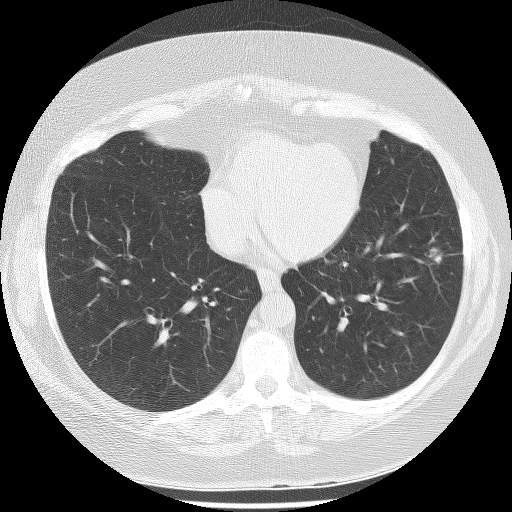
Axial slice from a low-dose chest CT screening exam. Baseline annual screen. Lung window (W 1500 / L -600 HU). 2.5 mm slice thickness. Lung (sharp) reconstruction kernel (BONE). Slice 136 of 233 in the series. Female participant, aged 56 years at enrolment. Former smoker at enrolment.
Expert reader's lesion annotation, bounding box (x1, y1, x2, y2) in pixels: (388, 222, 465, 287). The exam's reader record, not a measurement of the box and not confirmed to be the same lesion: non-calcified nodule or mass ≥4 mm, left lower lobe, 22 × 17 mm, spiculated (stellate) margins, soft tissue attenuation. Lung cancer was diagnosed 63 days after this screen: bronchiolo-alveolar adenocarcinoma, NOS, left lower lobe, stage IA (AJCC 6th edition), 18 mm at pathology.